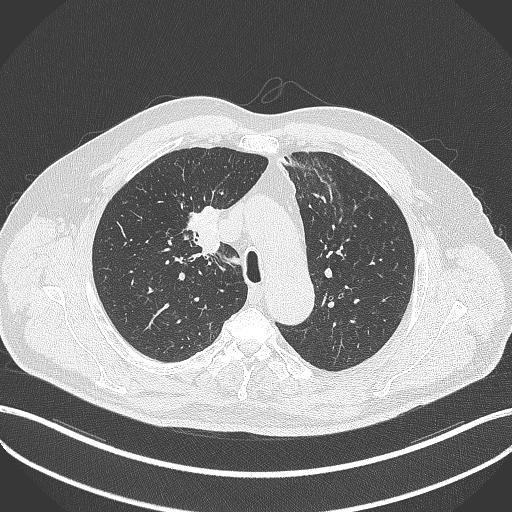
Chest CT, one axial slice. Position 285 of 411 along the scan axis. Reconstruction kernel B70f. 120 kVp. Lung window (W 1500 / L -600 HU). 512 × 512 image matrix. Patient: male, 60 years. From the clinical record (not read from this slice): clinical TNM (as recorded): T1b N1 M0.
Outlined on this slice (rectangle marked by the reading radiologist):
- lung tumour (recorded histology: squamous cell carcinoma): box from (x=181, y=196) to (x=226, y=266) px